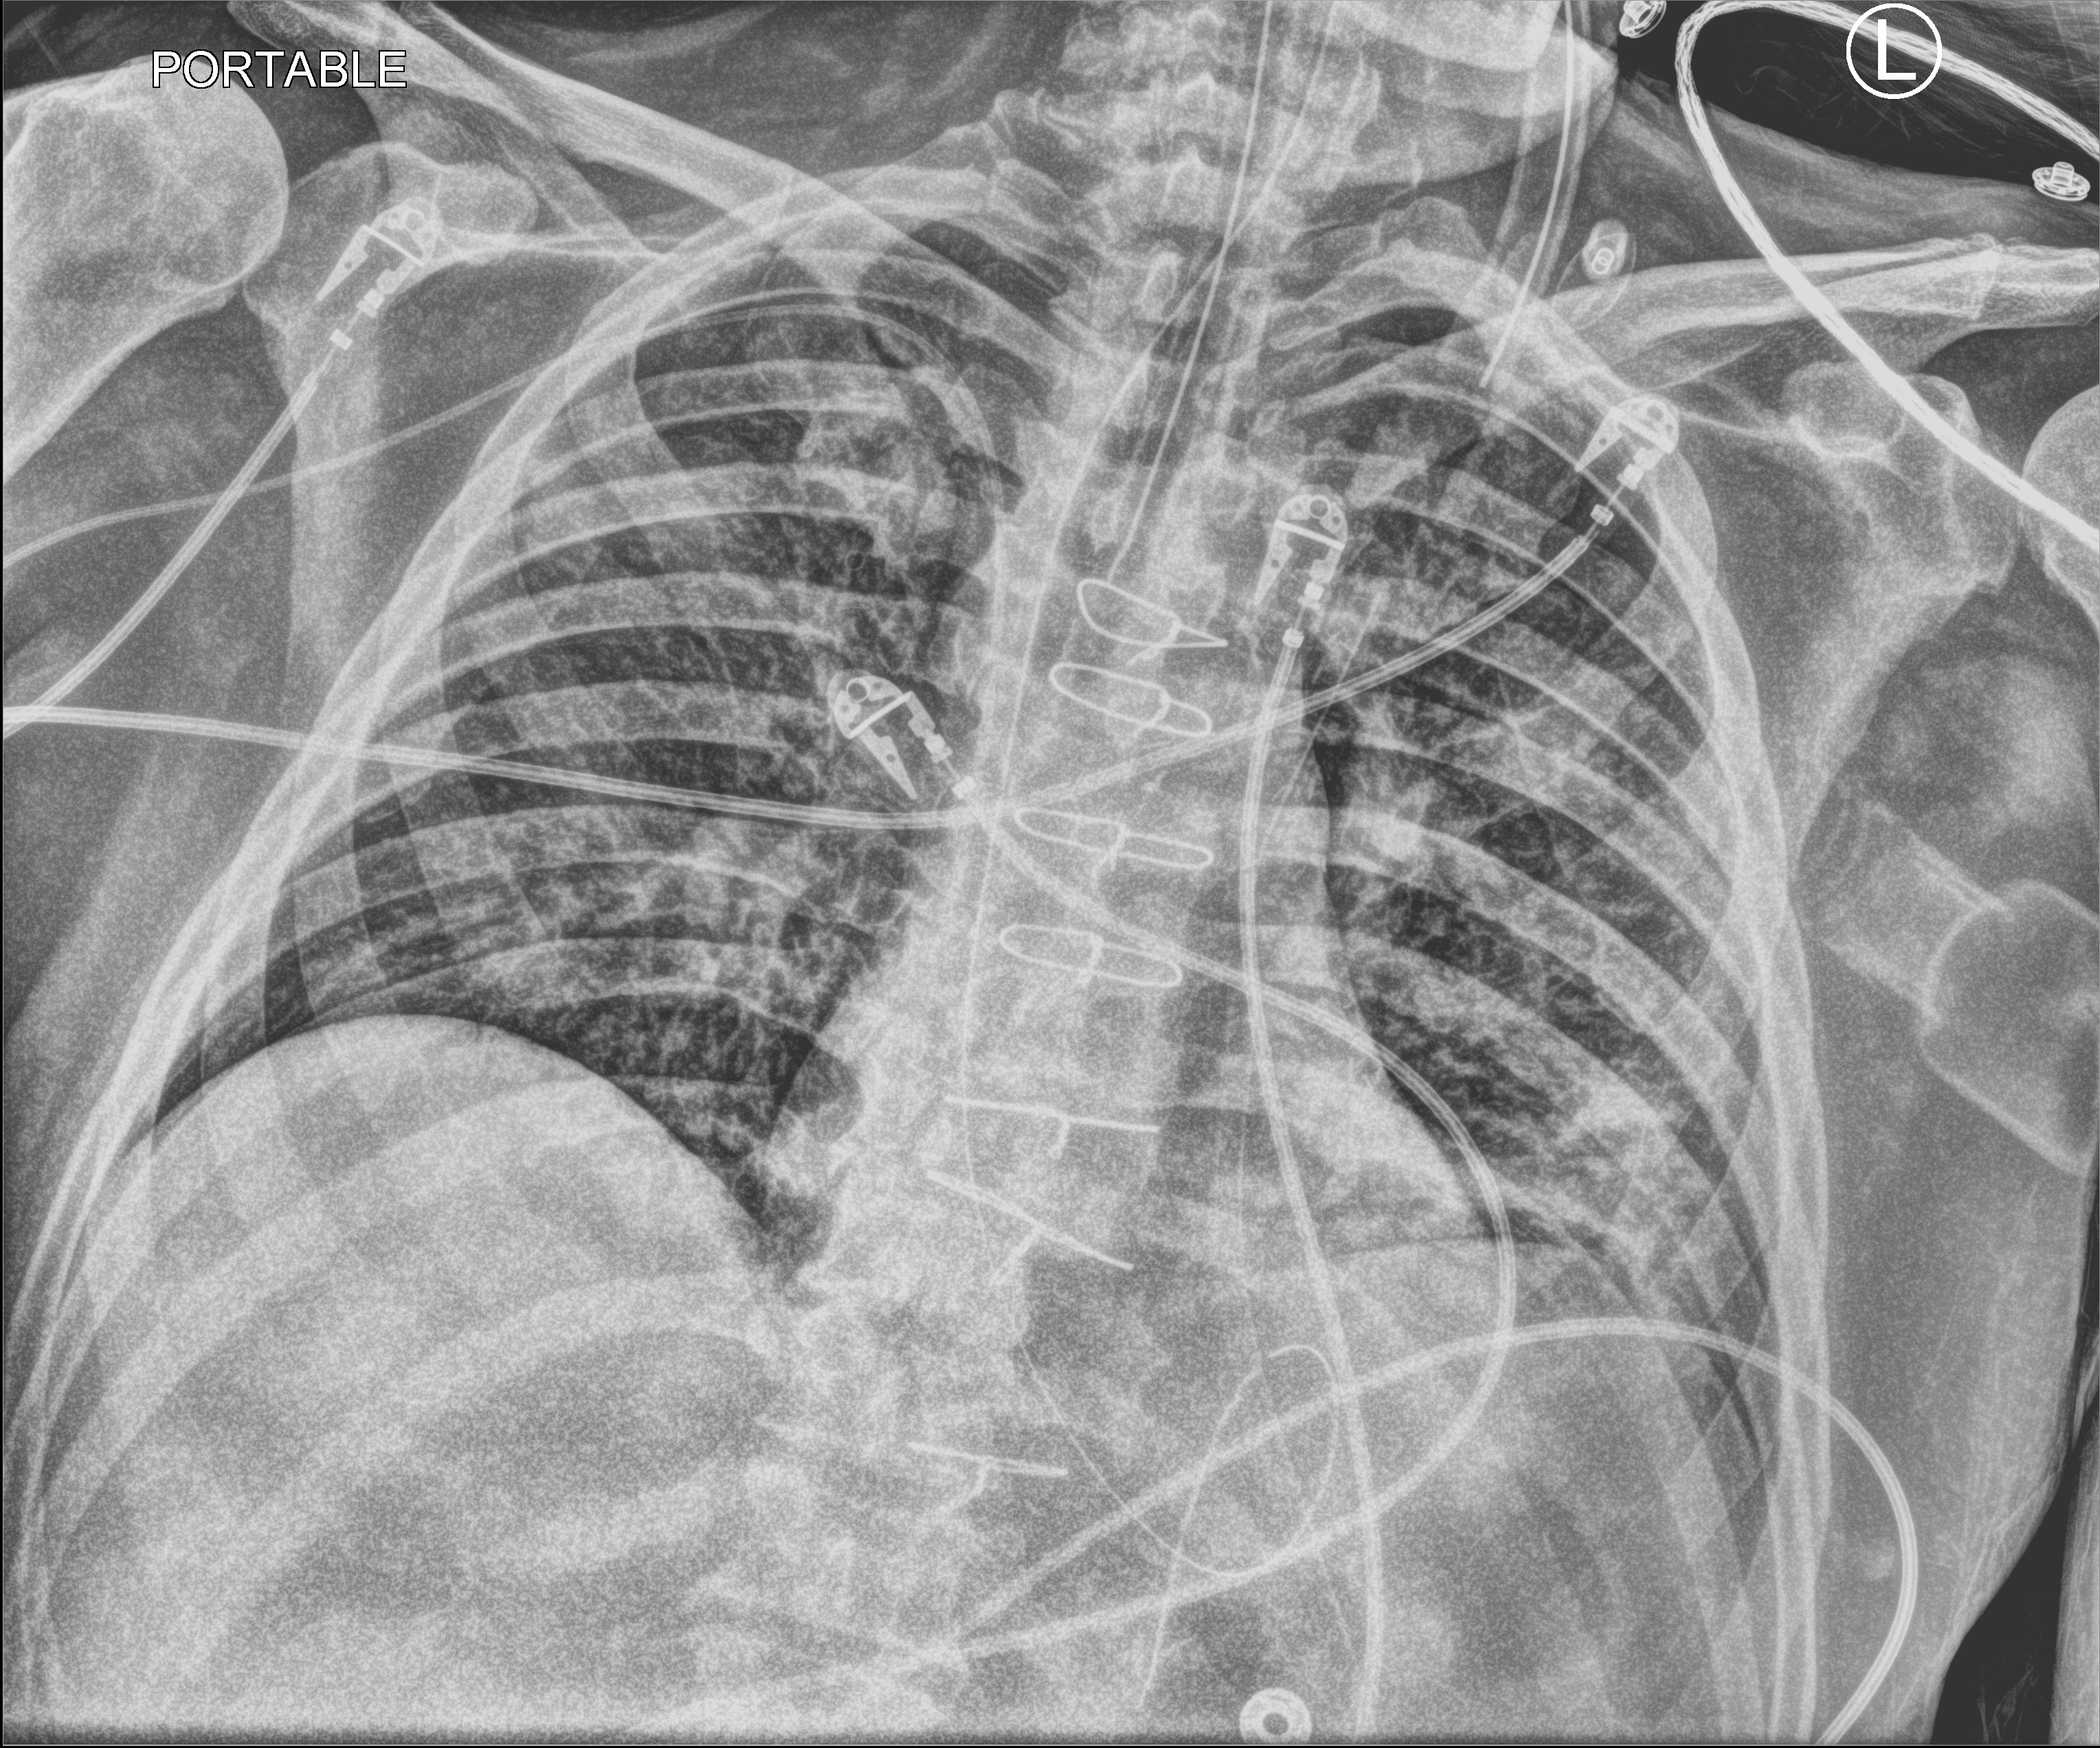
Portable chest radiograph; anteroposterior (AP) projection. Male patient hospitalised with COVID-19, age 60–74 years.
From the hospital-stay record, not from the radiograph (when in the stay this image was taken is not recorded): COPD (admission record): no; mechanically ventilated during this hospital stay: yes.